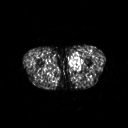
FDG PET of an extremity soft-tissue mass (from a PET/CT study), one axial slice. Slice 239 of 311 in the series (ordered by position). 3.27 mm slice thickness. 128 × 128 image matrix, field of view 500 × 500 mm. Patient: male, 29 years. From the clinical record (not read from this slice): histological type: mixoid liposarcoma; grade: low; site of the primary tumour: left thigh.
Structures marked on this image (expert contour drawn on MRI and transferred to this co-registered scan by the dataset authors):
- gross tumour volume (mass): box from (x=70, y=53) to (x=82, y=70) px